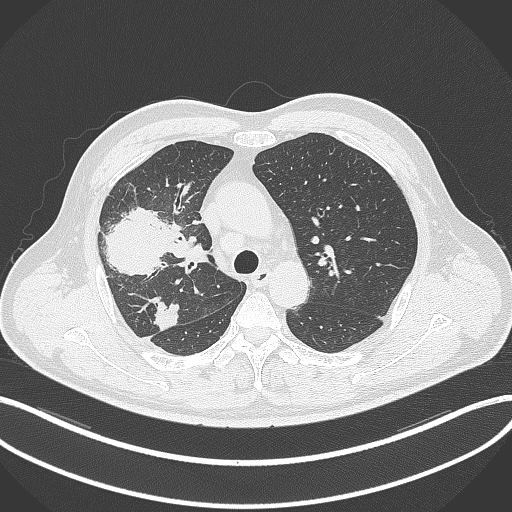
Chest CT, one axial slice; 120 kVp; lung window (W 1500 / L -600 HU); 512 × 512 image matrix, field of view 400 × 400 mm. Patient: male, 55 years. From the clinical record (not read from this slice): clinical TNM (as recorded): T3 N2 M1.
Outlined on this slice (bounding box drawn by a radiologist):
- lung tumour (recorded histology: adenocarcinoma): bounding box [x1, y1, x2, y2] px = [95, 208, 182, 280]